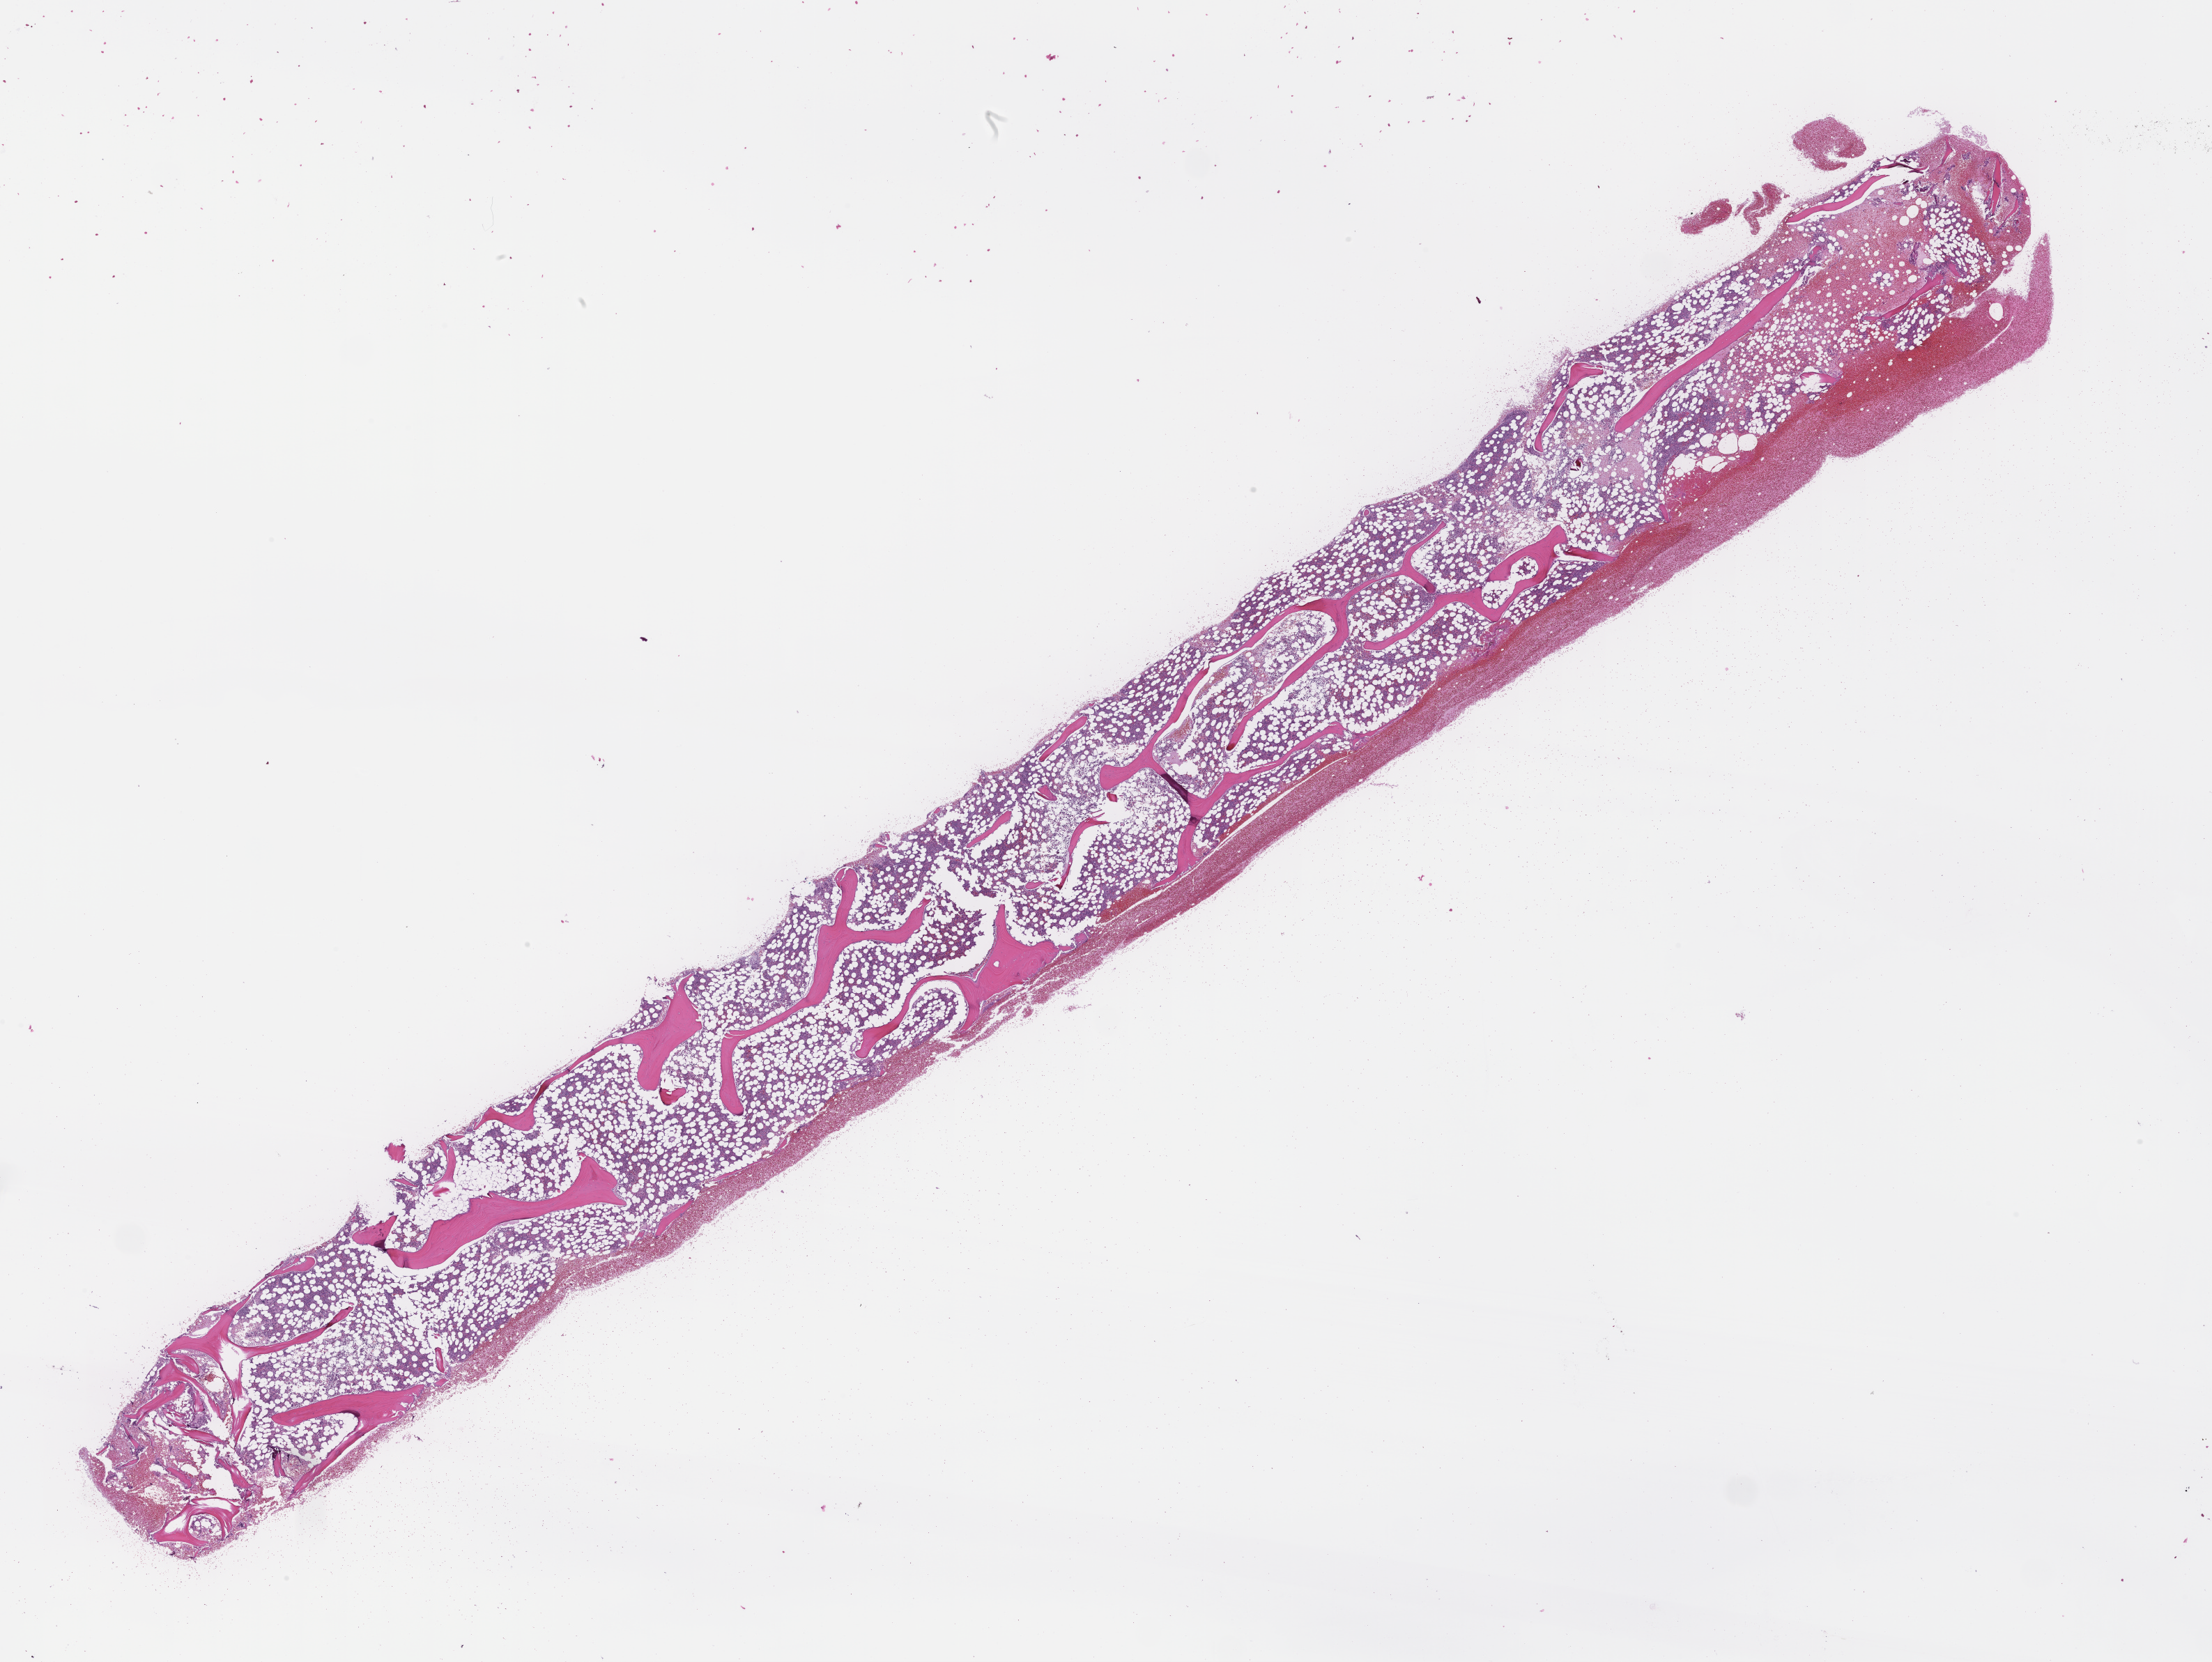
Digitized H&E-stained section, low-resolution overview of the scanned area, about 25.6 x 19.3 mm; formalin-fixed, paraffin-embedded (FFPE) tissue; tissue site: bone marrow; archival tissue. Patient: male.
This section: primary tumour tissue. Diagnosis: Plasma Cell Myeloma.